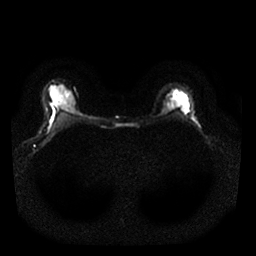
Breast MRI, one axial slice. Diffusion-weighted series; image 2 of 4 stored at this slice position (different b-values; order by instance number). 1.5 T. 4 mm slice thickness. 256 × 256 image matrix, field of view 320 × 320 mm. Female patient.
Structures marked on this image (outlined manually by an expert reader):
- tumour on diffusion-weighted imaging: bounding box (x1, y1, x2, y2) in pixels: (162, 106, 168, 110)